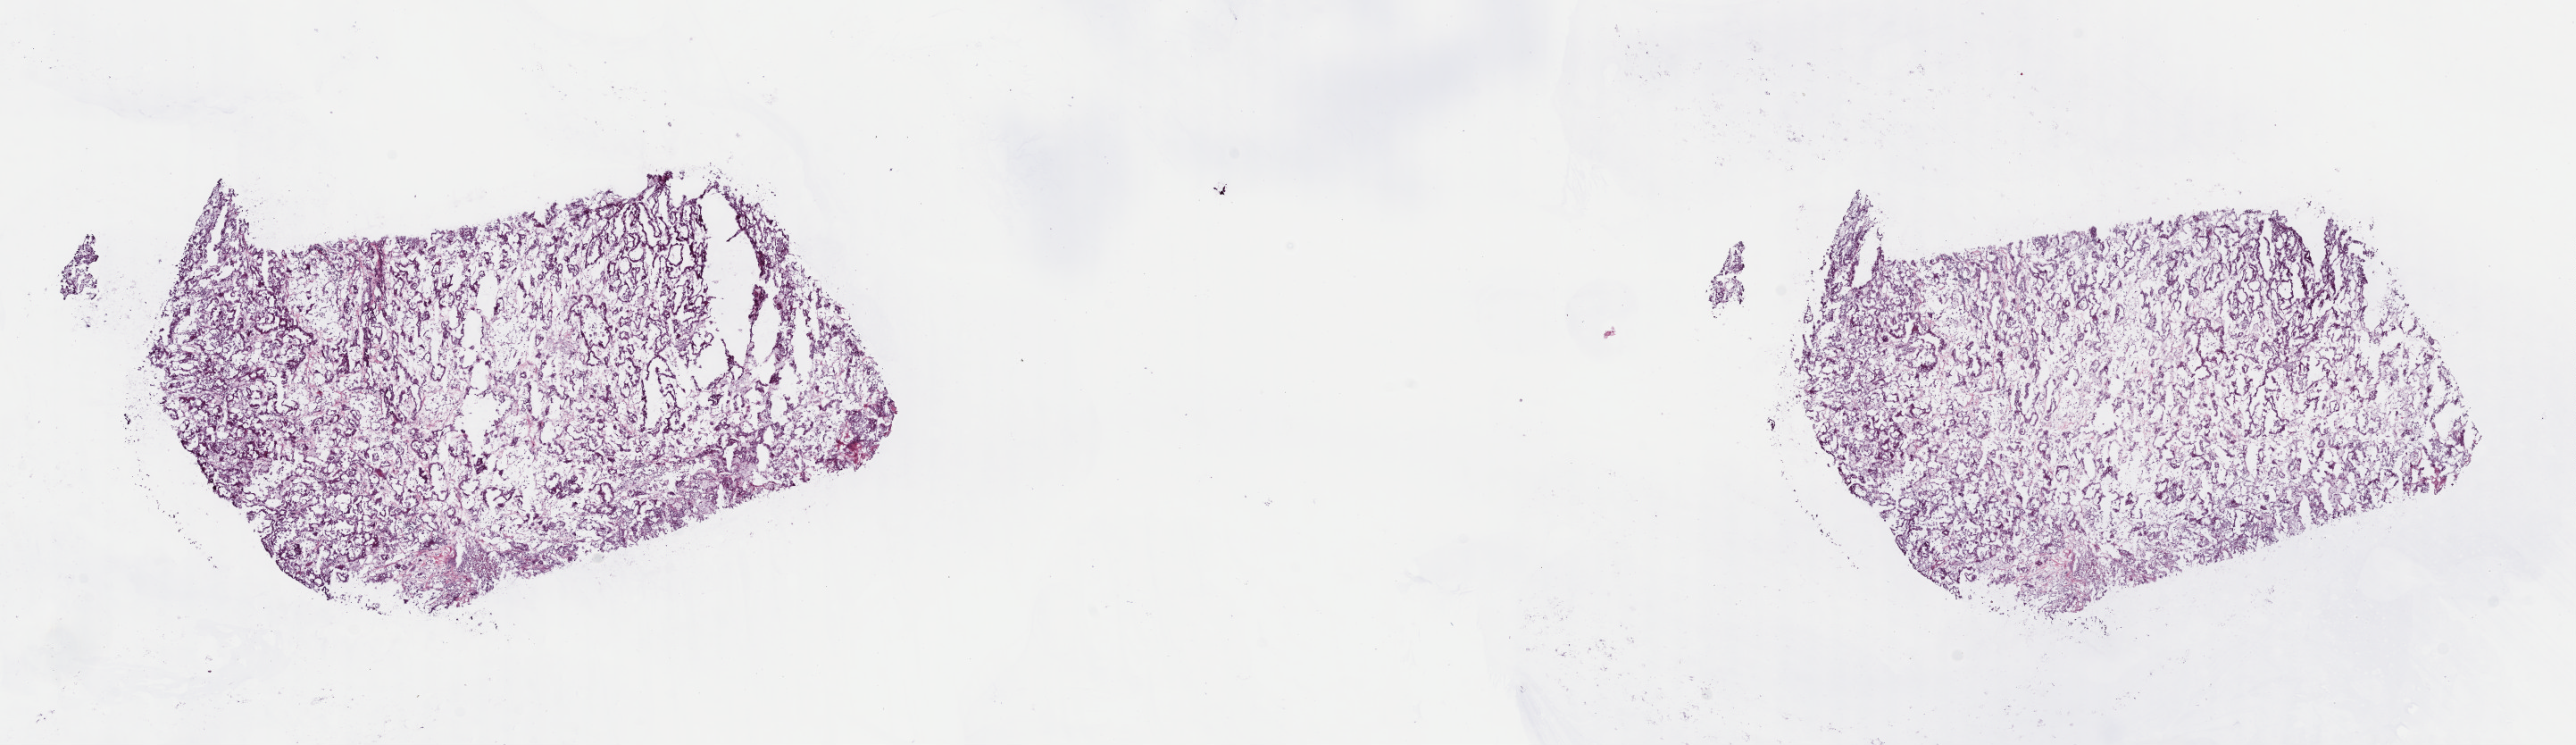
Whole-slide histology image, Hematoxylin and eosin (H&E) stained — whole scanned area (about 22.8 x 6.6 mm, from a 40x scan) shown as a low-resolution overview; frozen section; primary tumour sample from the kidney. Male, age 58 years at initial diagnosis.
Pathologic diagnosis: Papillary adenocarcinoma, NOS.